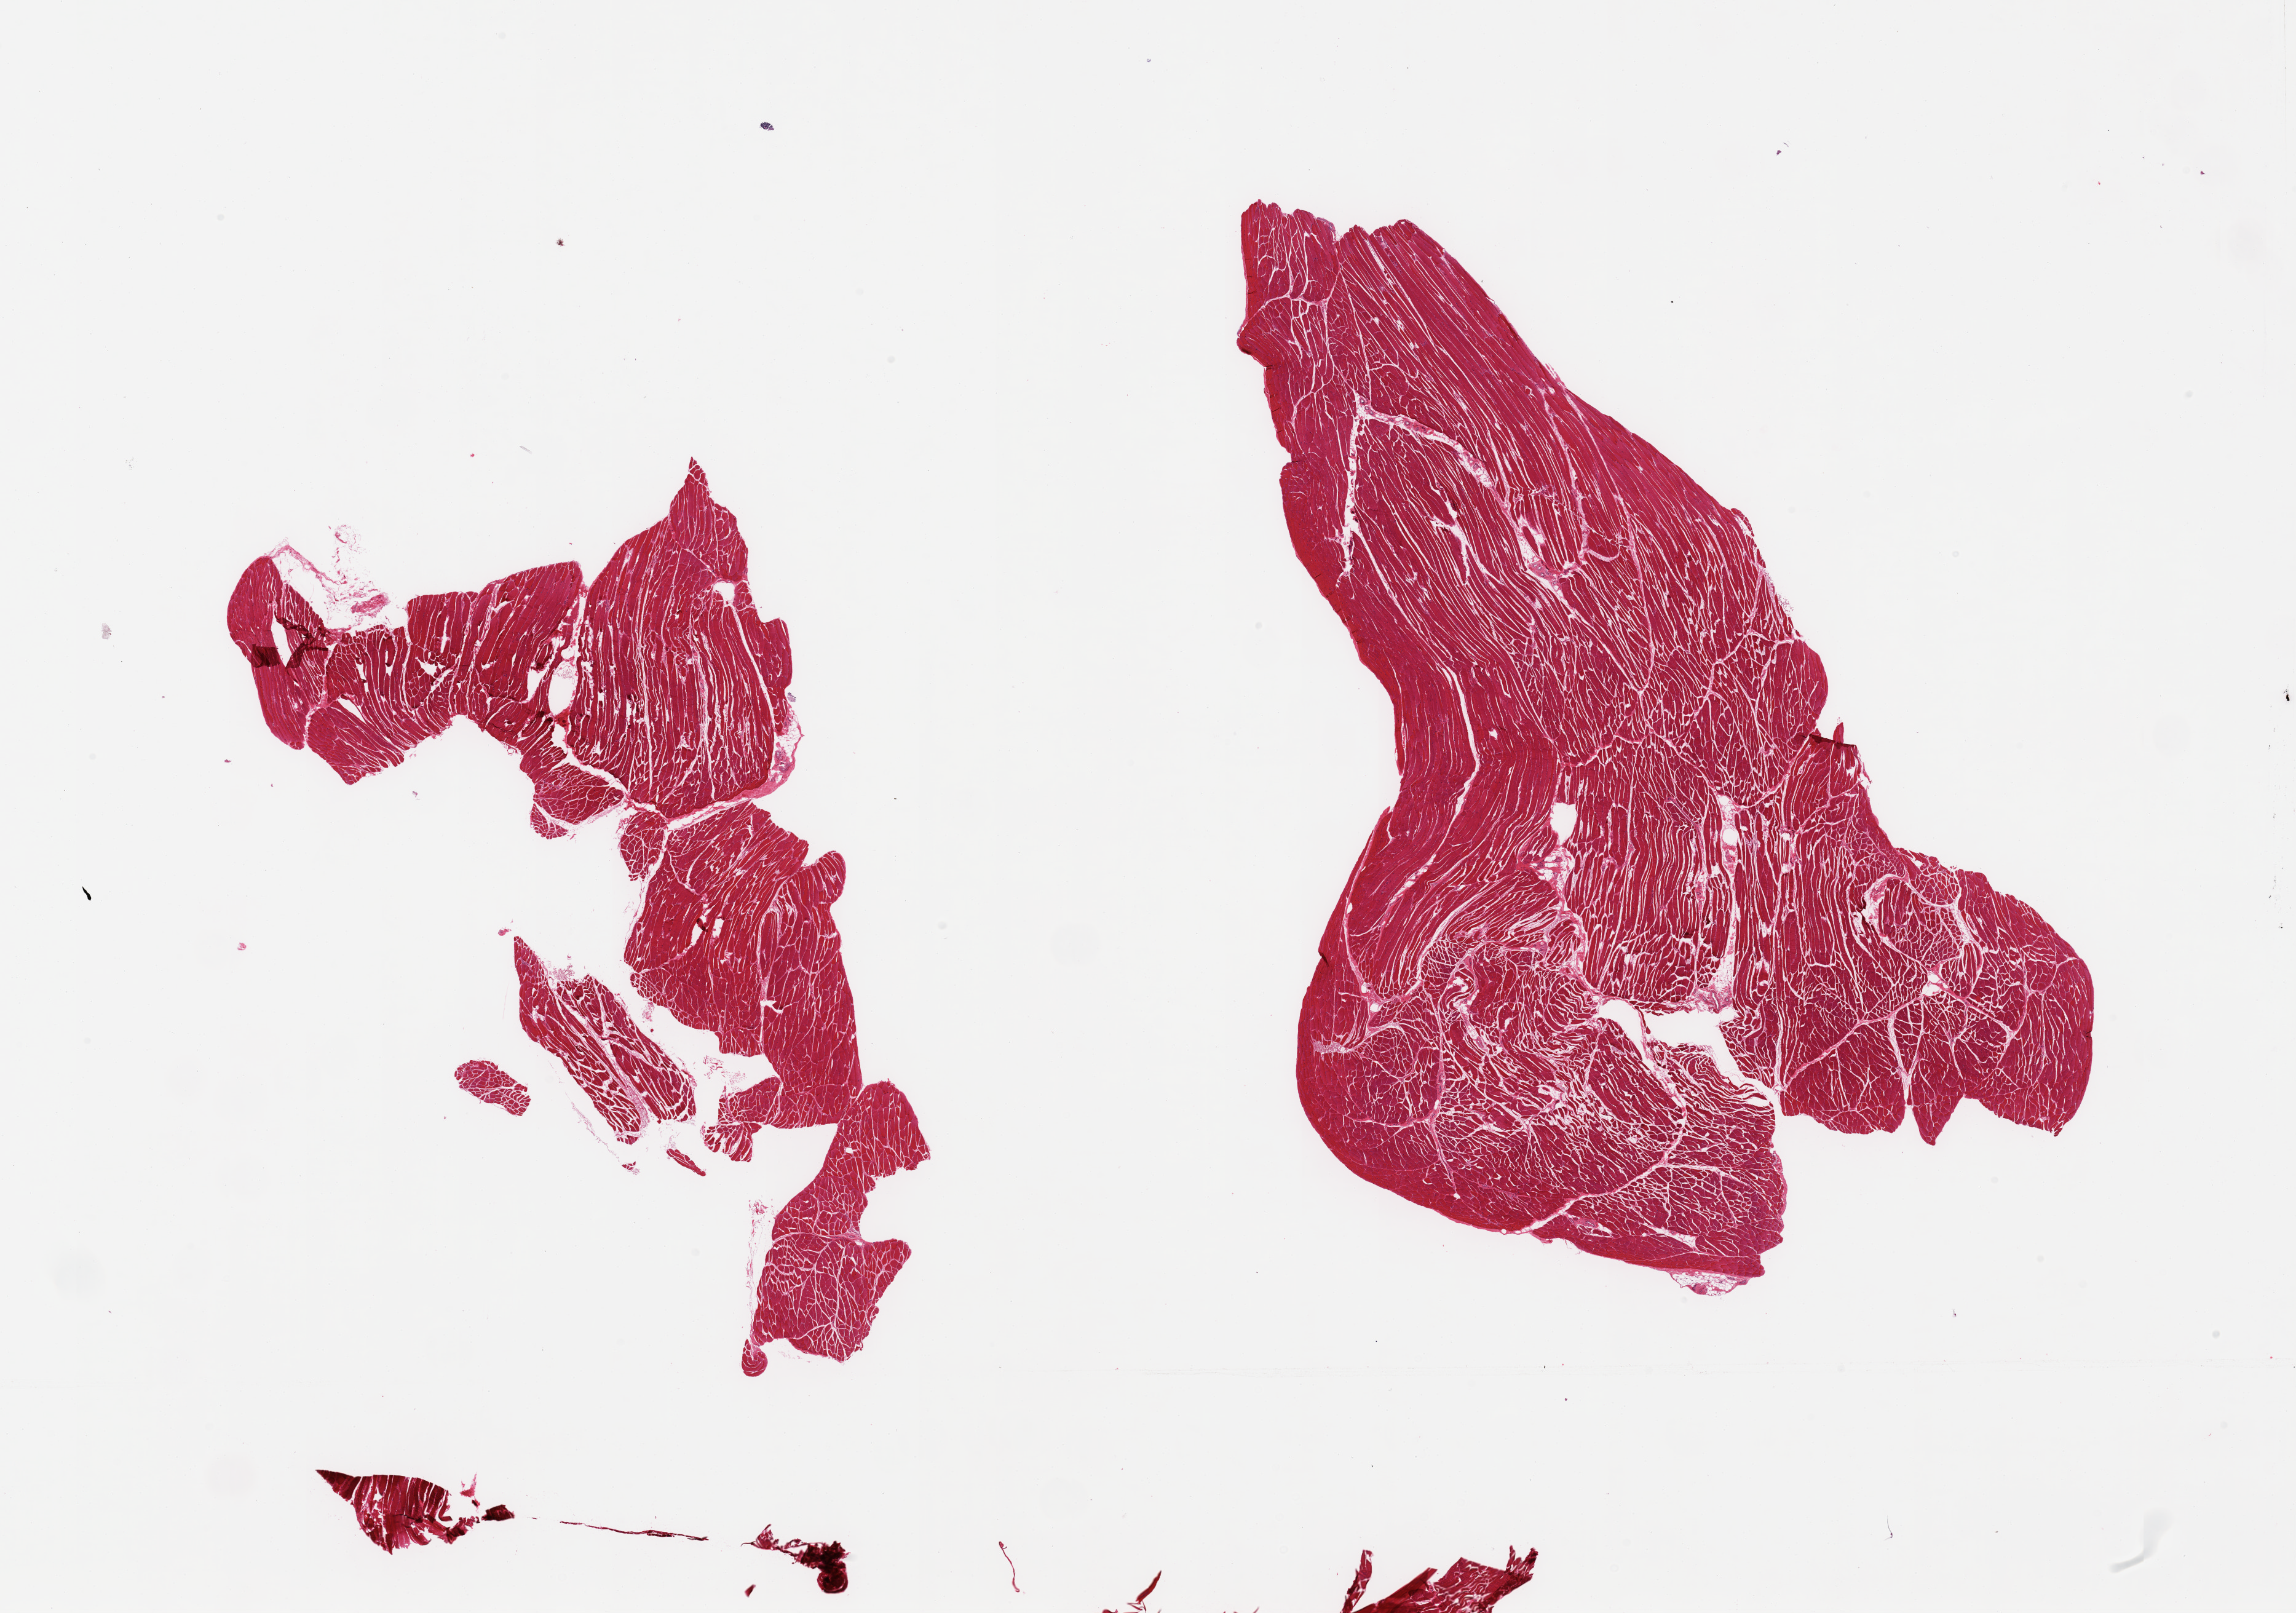
H&E whole-slide image — shown as a low-resolution overview of the whole scanned area (about 29.5 x 20.7 mm), PAXgene-fixed, paraffin-embedded tissue, section of skeletal muscle (target tissue), donor tissue sample. Donor: male.
Review note (as recorded): 2 pieces; minimal stroma.